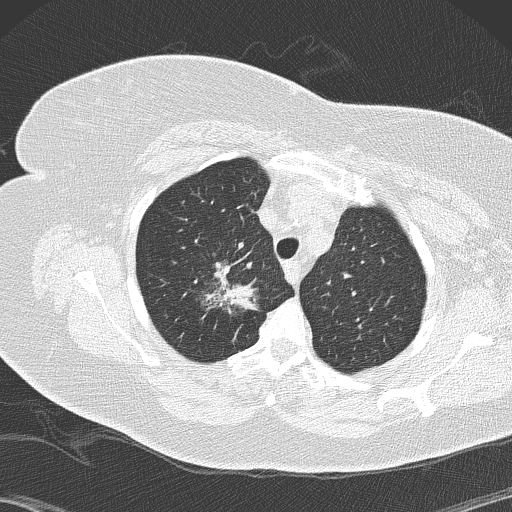
Axial slice from a low-dose chest CT screening exam. Second annual screen. Lung window (W 1500 / L -600 HU). 2 mm slice thickness. Lung (sharp) reconstruction kernel (B50f). Female, age 72 years at enrolment. Former smoker at enrolment.
Lesion marked by an expert reader, box from (x=180, y=242) to (x=263, y=328) px. The screening reader recorded 4 non-calcified nodules or masses ≥4 mm on this exam (right lower lobe, right lower lobe, right lower lobe, right upper lobe); which of them this box marks is not recorded.